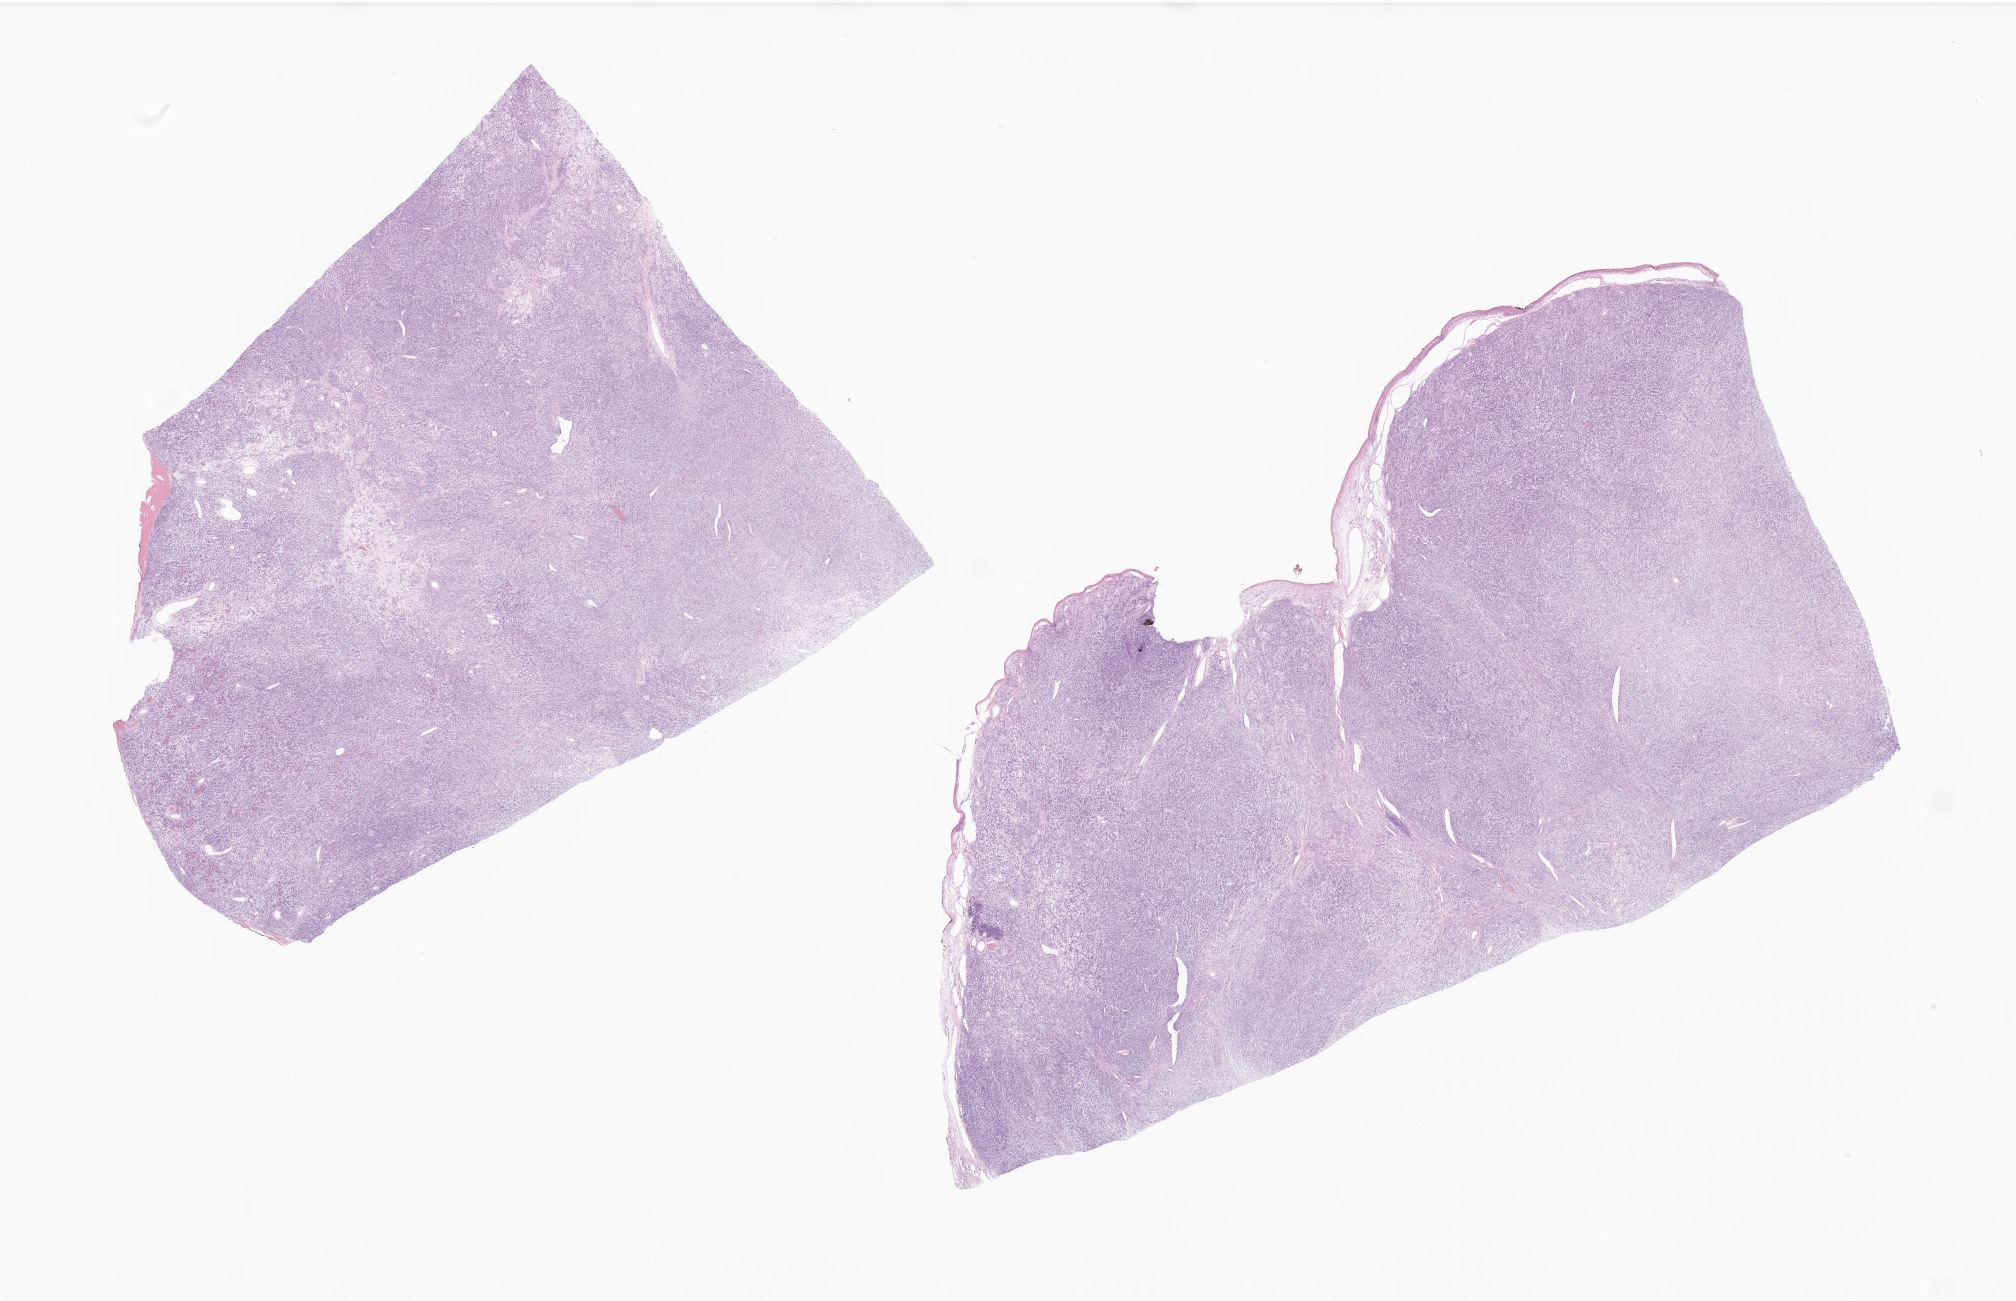
Haematoxylin and eosin whole-slide image of tumor tissue from the ovary, whole scanned area (about 34.0 x 21.9 mm) shown as a low-resolution overview; formalin-fixed paraffin-embedded section. Patient: female, age 137 months (11 years 5 months).
Diagnosis (ICD-O-3 morphology term): Small cell carcinoma, NOS.